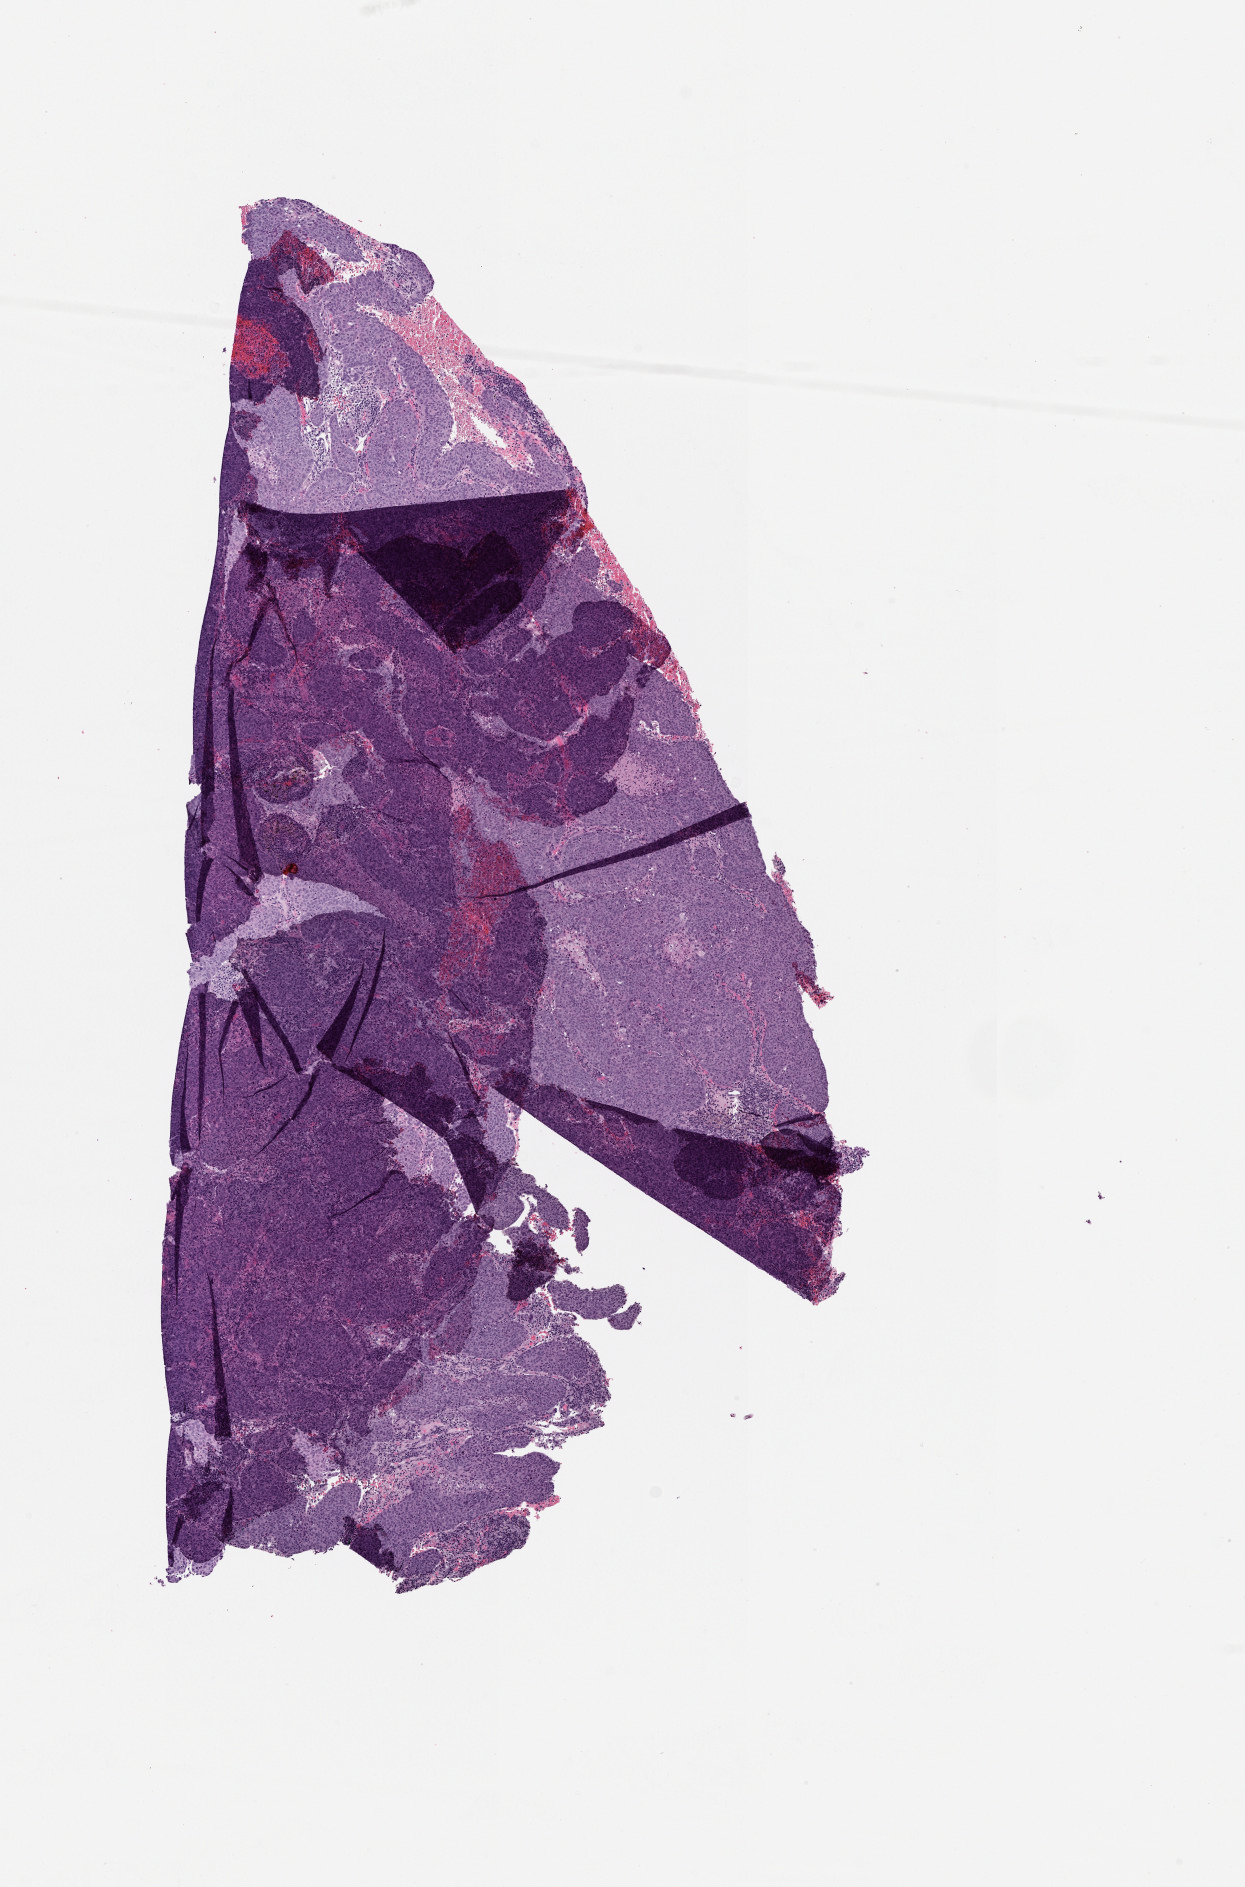
H&E whole-slide image, whole scanned area (about 5.0 x 7.6 mm, slide scanned at 20x) shown as a low-resolution overview, lung, tumour tissue. Patient: female, age 71 years.
Patient diagnosis (cohort enrolment): squamous cell carcinoma (lung).